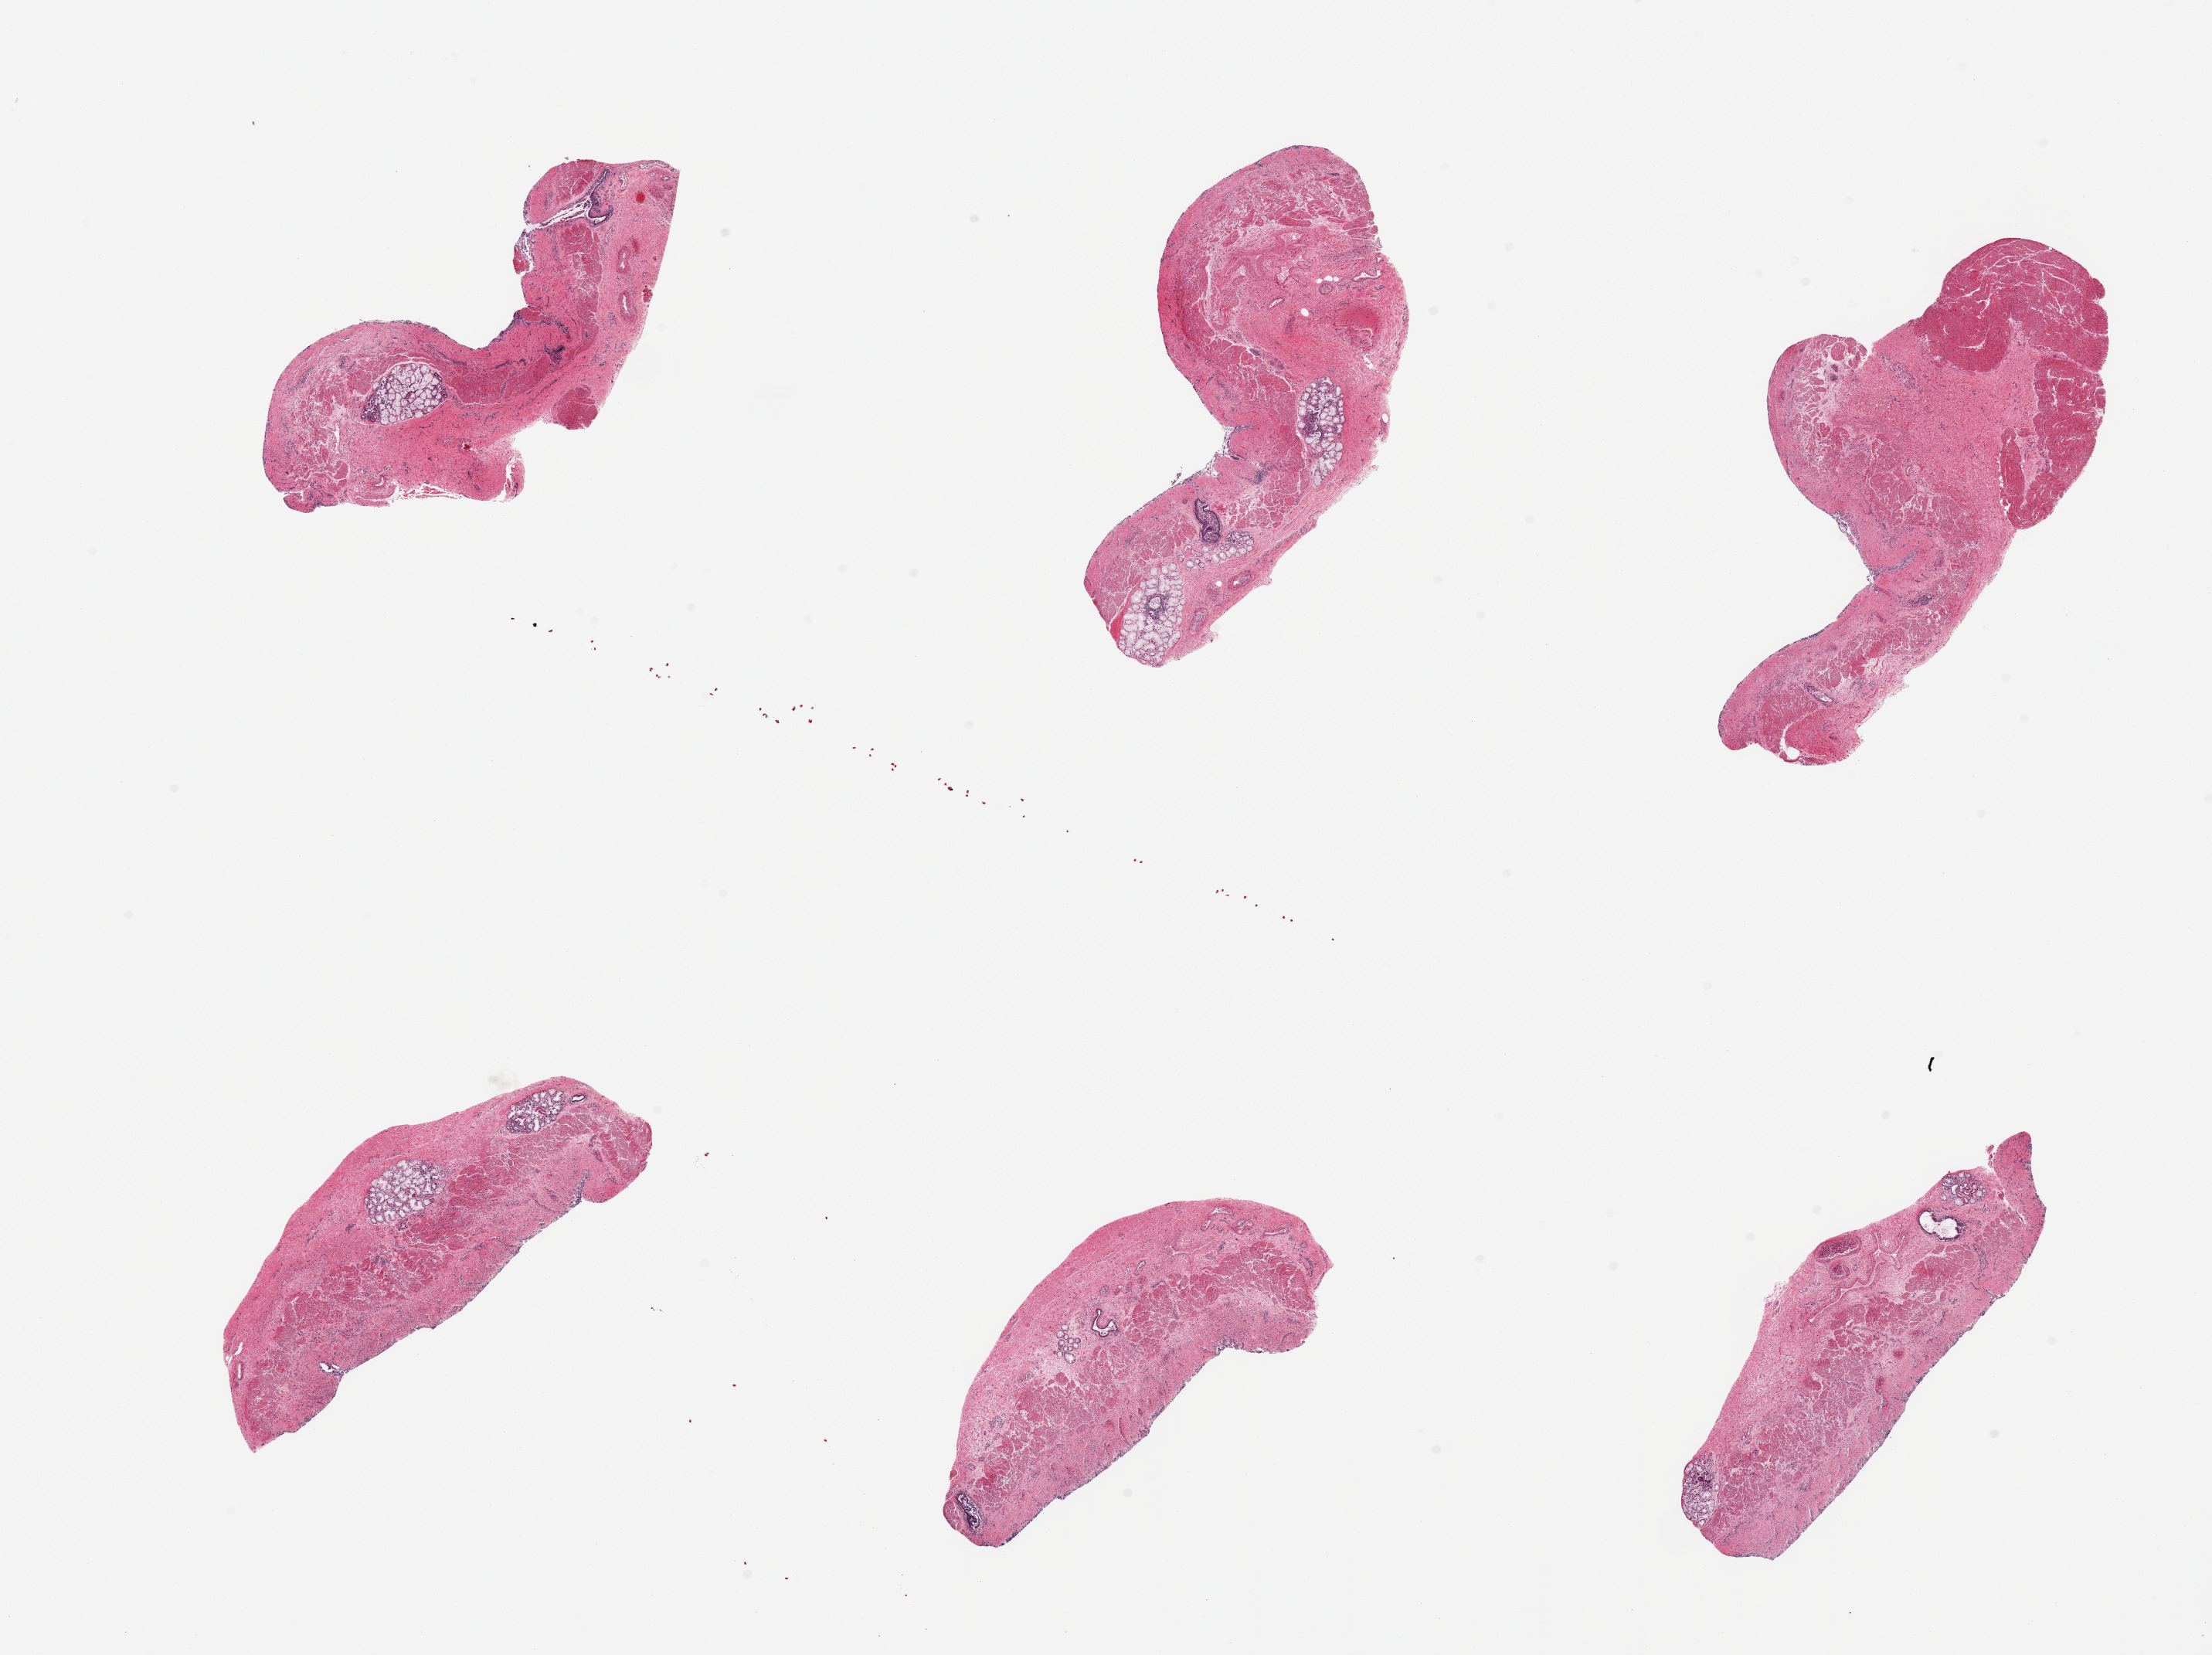
Hematoxylin and eosin (H&E) whole-slide image — shown as a low-resolution overview of the whole scanned area (about 22.6 x 16.9 mm), PAXgene-fixed paraffin-embedded (PFPE) section, section of esophageal mucous membrane (target tissue), tissue donor sample. Male donor.
Reviewer comment on this tissue sample: 6 pieces, squamous mucosa competely sloughed; residual submucosal mucus glands present.